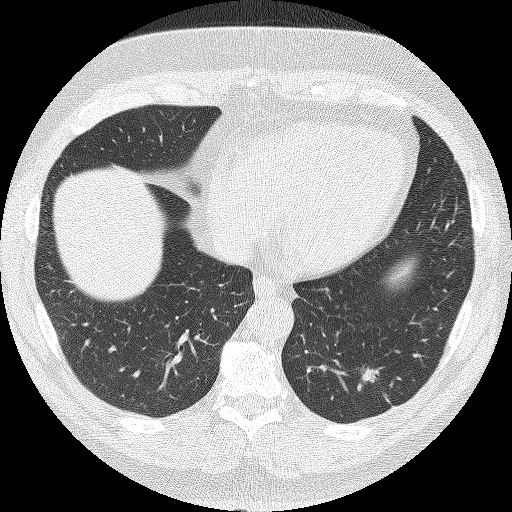
Low-dose screening chest CT, axial slice, baseline screening round, lung window (W 1500 / L -600 HU), 2 mm slice thickness, 120 kVp. Male, age 62 years at enrolment. Current smoker at enrolment.
- Lesion marked by an expert reader, bounding box [x1, y1, x2, y2] px = [348, 351, 406, 399].
- The screening reader recorded 2 non-calcified nodules or masses ≥4 mm on this exam; which of them this box marks is not recorded.
- Later outcome: lung cancer diagnosed 90 days after this screen — adenocarcinoma, NOS, left lower lobe, moderately differentiated (G2), stage IA (AJCC 6th edition), 30 mm at pathology.